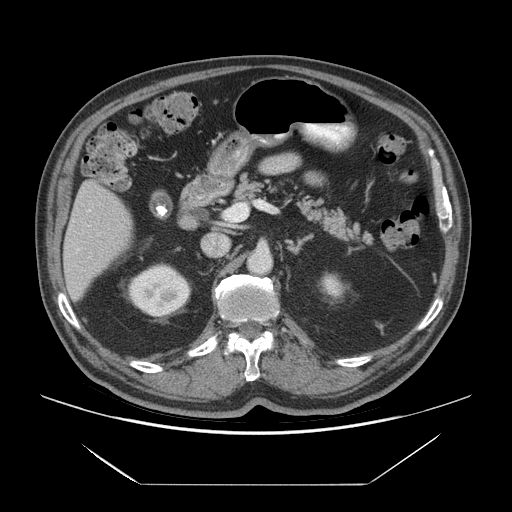
Contrast-enhanced abdominal CT (liver protocol), one axial slice; slice 30 of 75 in the series (ordered by position); reconstruction kernel STANDARD; soft-tissue window (W 400 / L 40 HU); 512 × 512 image matrix, field of view 420 × 420 mm. From the clinical record (not read from this slice): diagnosis: hepatocellular carcinoma (patient treated with transarterial chemoembolisation; whether this scan precedes or follows treatment is not stated here); TNM stage (as recorded): Stage-I; Child-Pugh class: A; tumour differentiation: well differentiated.
Structures marked on this image (semi-automatic segmentation, software-assisted and operator-edited):
- liver parenchyma outside the tumour (the mass and vessels are separate outlines, so this box may not span the whole liver): box from (x=62, y=180) to (x=132, y=301) px
- liver vessels: (x=76, y=209)–(x=91, y=252)